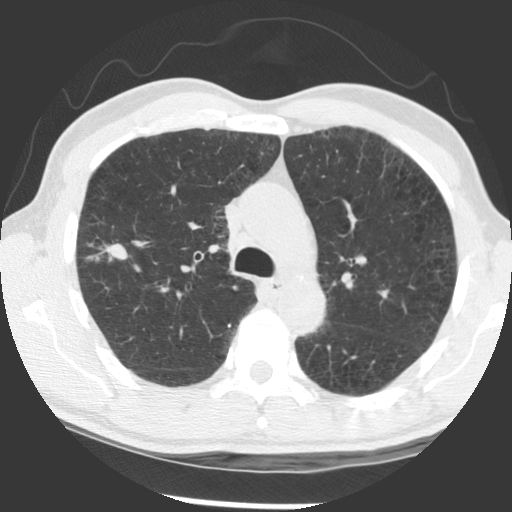
Low-dose screening chest CT, axial slice, baseline annual screen, lung window (W 1500 / L -600 HU), slice 96 of 140 in the series, 512 × 512 image matrix, field of view 321 × 321 mm. Male participant, aged 56 years at enrolment. Current smoker at enrolment.
• Expert reader's lesion annotation, box from (x=67, y=226) to (x=135, y=280) px.
• Screening reader's record for this exam (one nodule recorded; not confirmed to be the boxed lesion): non-calcified nodule or mass ≥4 mm, right upper lobe, 12 × 7 mm, spiculated (stellate) margins, soft tissue attenuation.
• Participant outcome: lung cancer diagnosed 676 days after this screen (after the second annual screen) — squamous cell carcinoma, NOS, right upper lobe, right middle lobe, moderately differentiated (G2), stage IB (AJCC 6th edition), 70 mm at pathology.